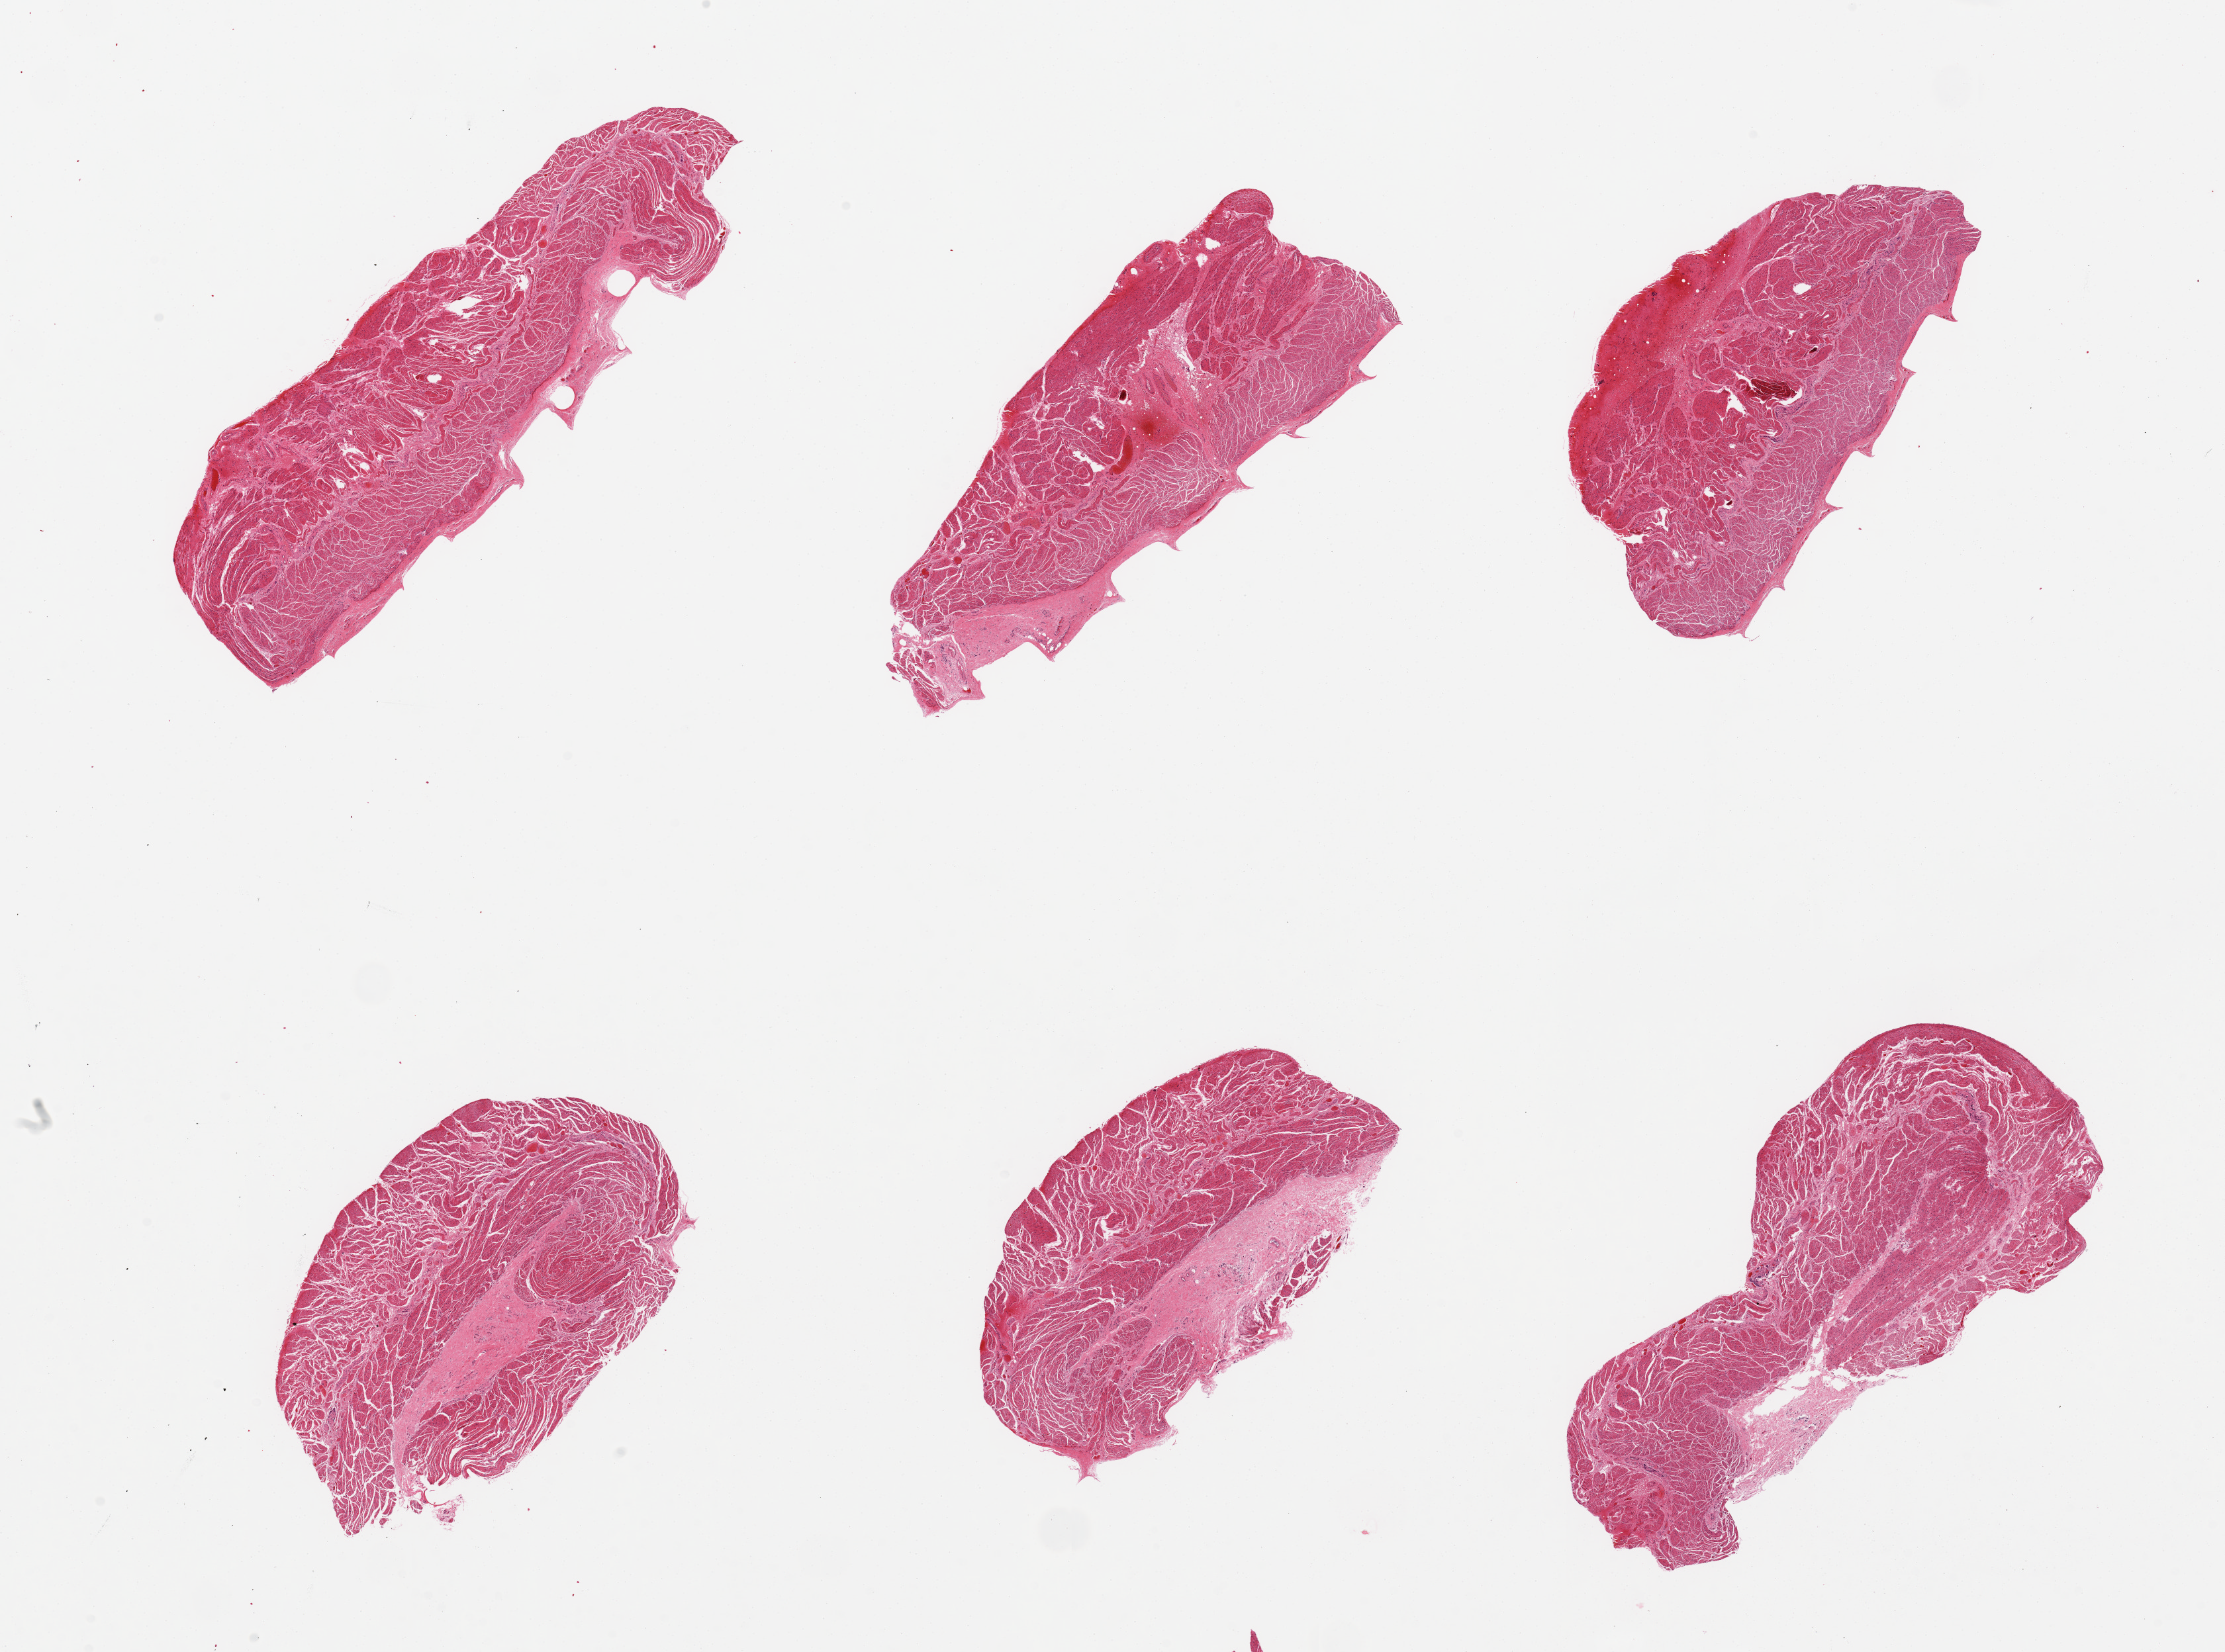
Haematoxylin and eosin whole-slide image, a low-resolution overview of the entire scanned area, about 26.6 x 19.7 mm, PAXgene-fixed paraffin-embedded (PFPE) section, section of esophageal muscle (target tissue), donor tissue sample. Female donor.
Pathologist's review note for this sample: 6 pieces, all muscularis, good specimens.